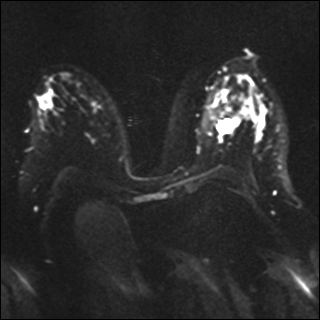
Breast MRI, one axial slice; position 20 of 41 along the scan axis; diffusion-weighted series; image 2 of 4 stored at this slice position (different b-values; order by instance number); 1.5 T; 320 × 320 image matrix, field of view 340 × 340 mm. Female patient.
Annotated regions visible in this slice (manually delineated by an expert):
- tumour on diffusion-weighted imaging: box from (x=217, y=119) to (x=232, y=133) px